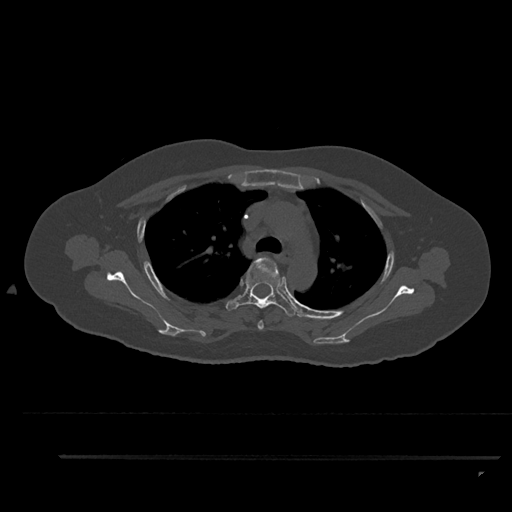
CT including the spine, one axial slice. Position 652 of 797 along the scan axis. Bone window (W 1800 / L 400 HU). 0.5 mm slice thickness. 512 × 512 image matrix, field of view 408 × 408 mm. Female patient, age 44 years. From the clinical record (not read from this slice): primary cancer: renal.
Annotated regions visible in this slice (semi-automatically segmented with operator editing):
- T3 vertebra: box from (x=258, y=320) to (x=264, y=330) px
- T4 vertebra: (x=226, y=257)–(x=297, y=317)